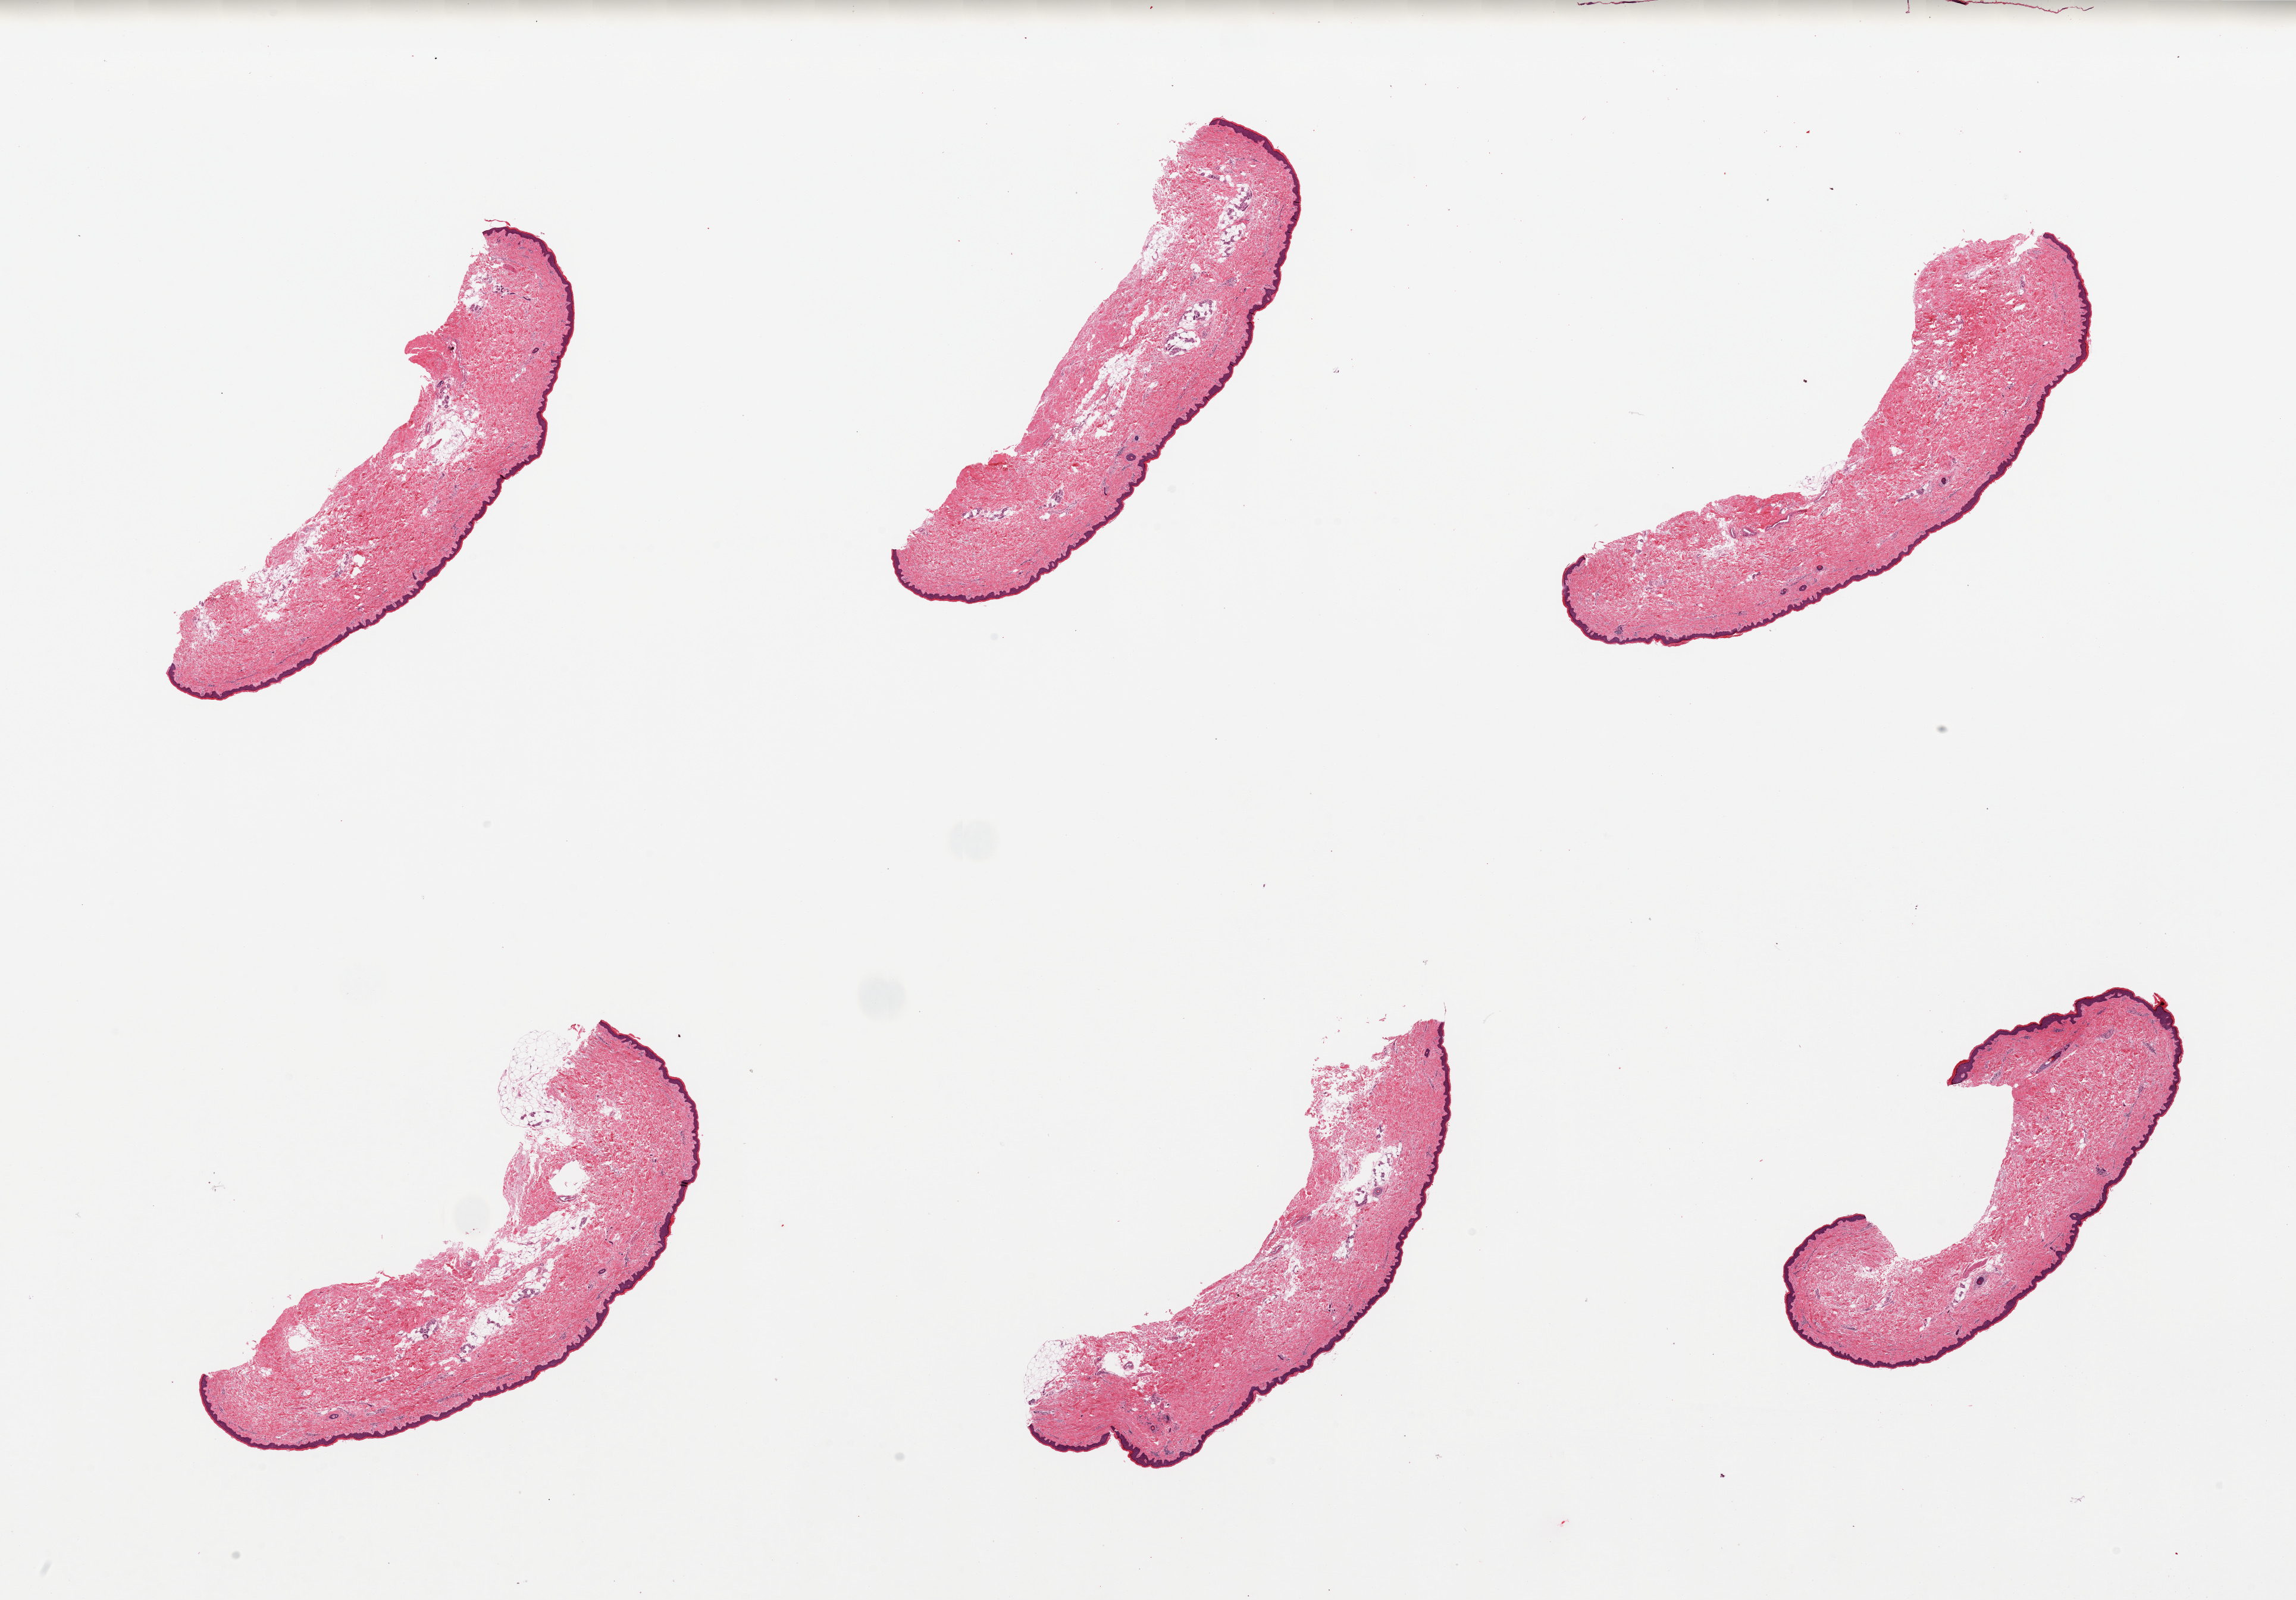
Haematoxylin and eosin whole-slide image, a low-resolution overview of the entire scanned area, about 30.5 x 21.3 mm (acquisition: 20x scan). PAXgene-fixed paraffin-embedded (PFPE) section. Section of skin of lower leg (target tissue). Donor tissue sample. Donor sex: female.
Reviewer comment on this tissue sample: 6 pieces, well trimmed, squamous epithelium measures 50-70 microns thick.